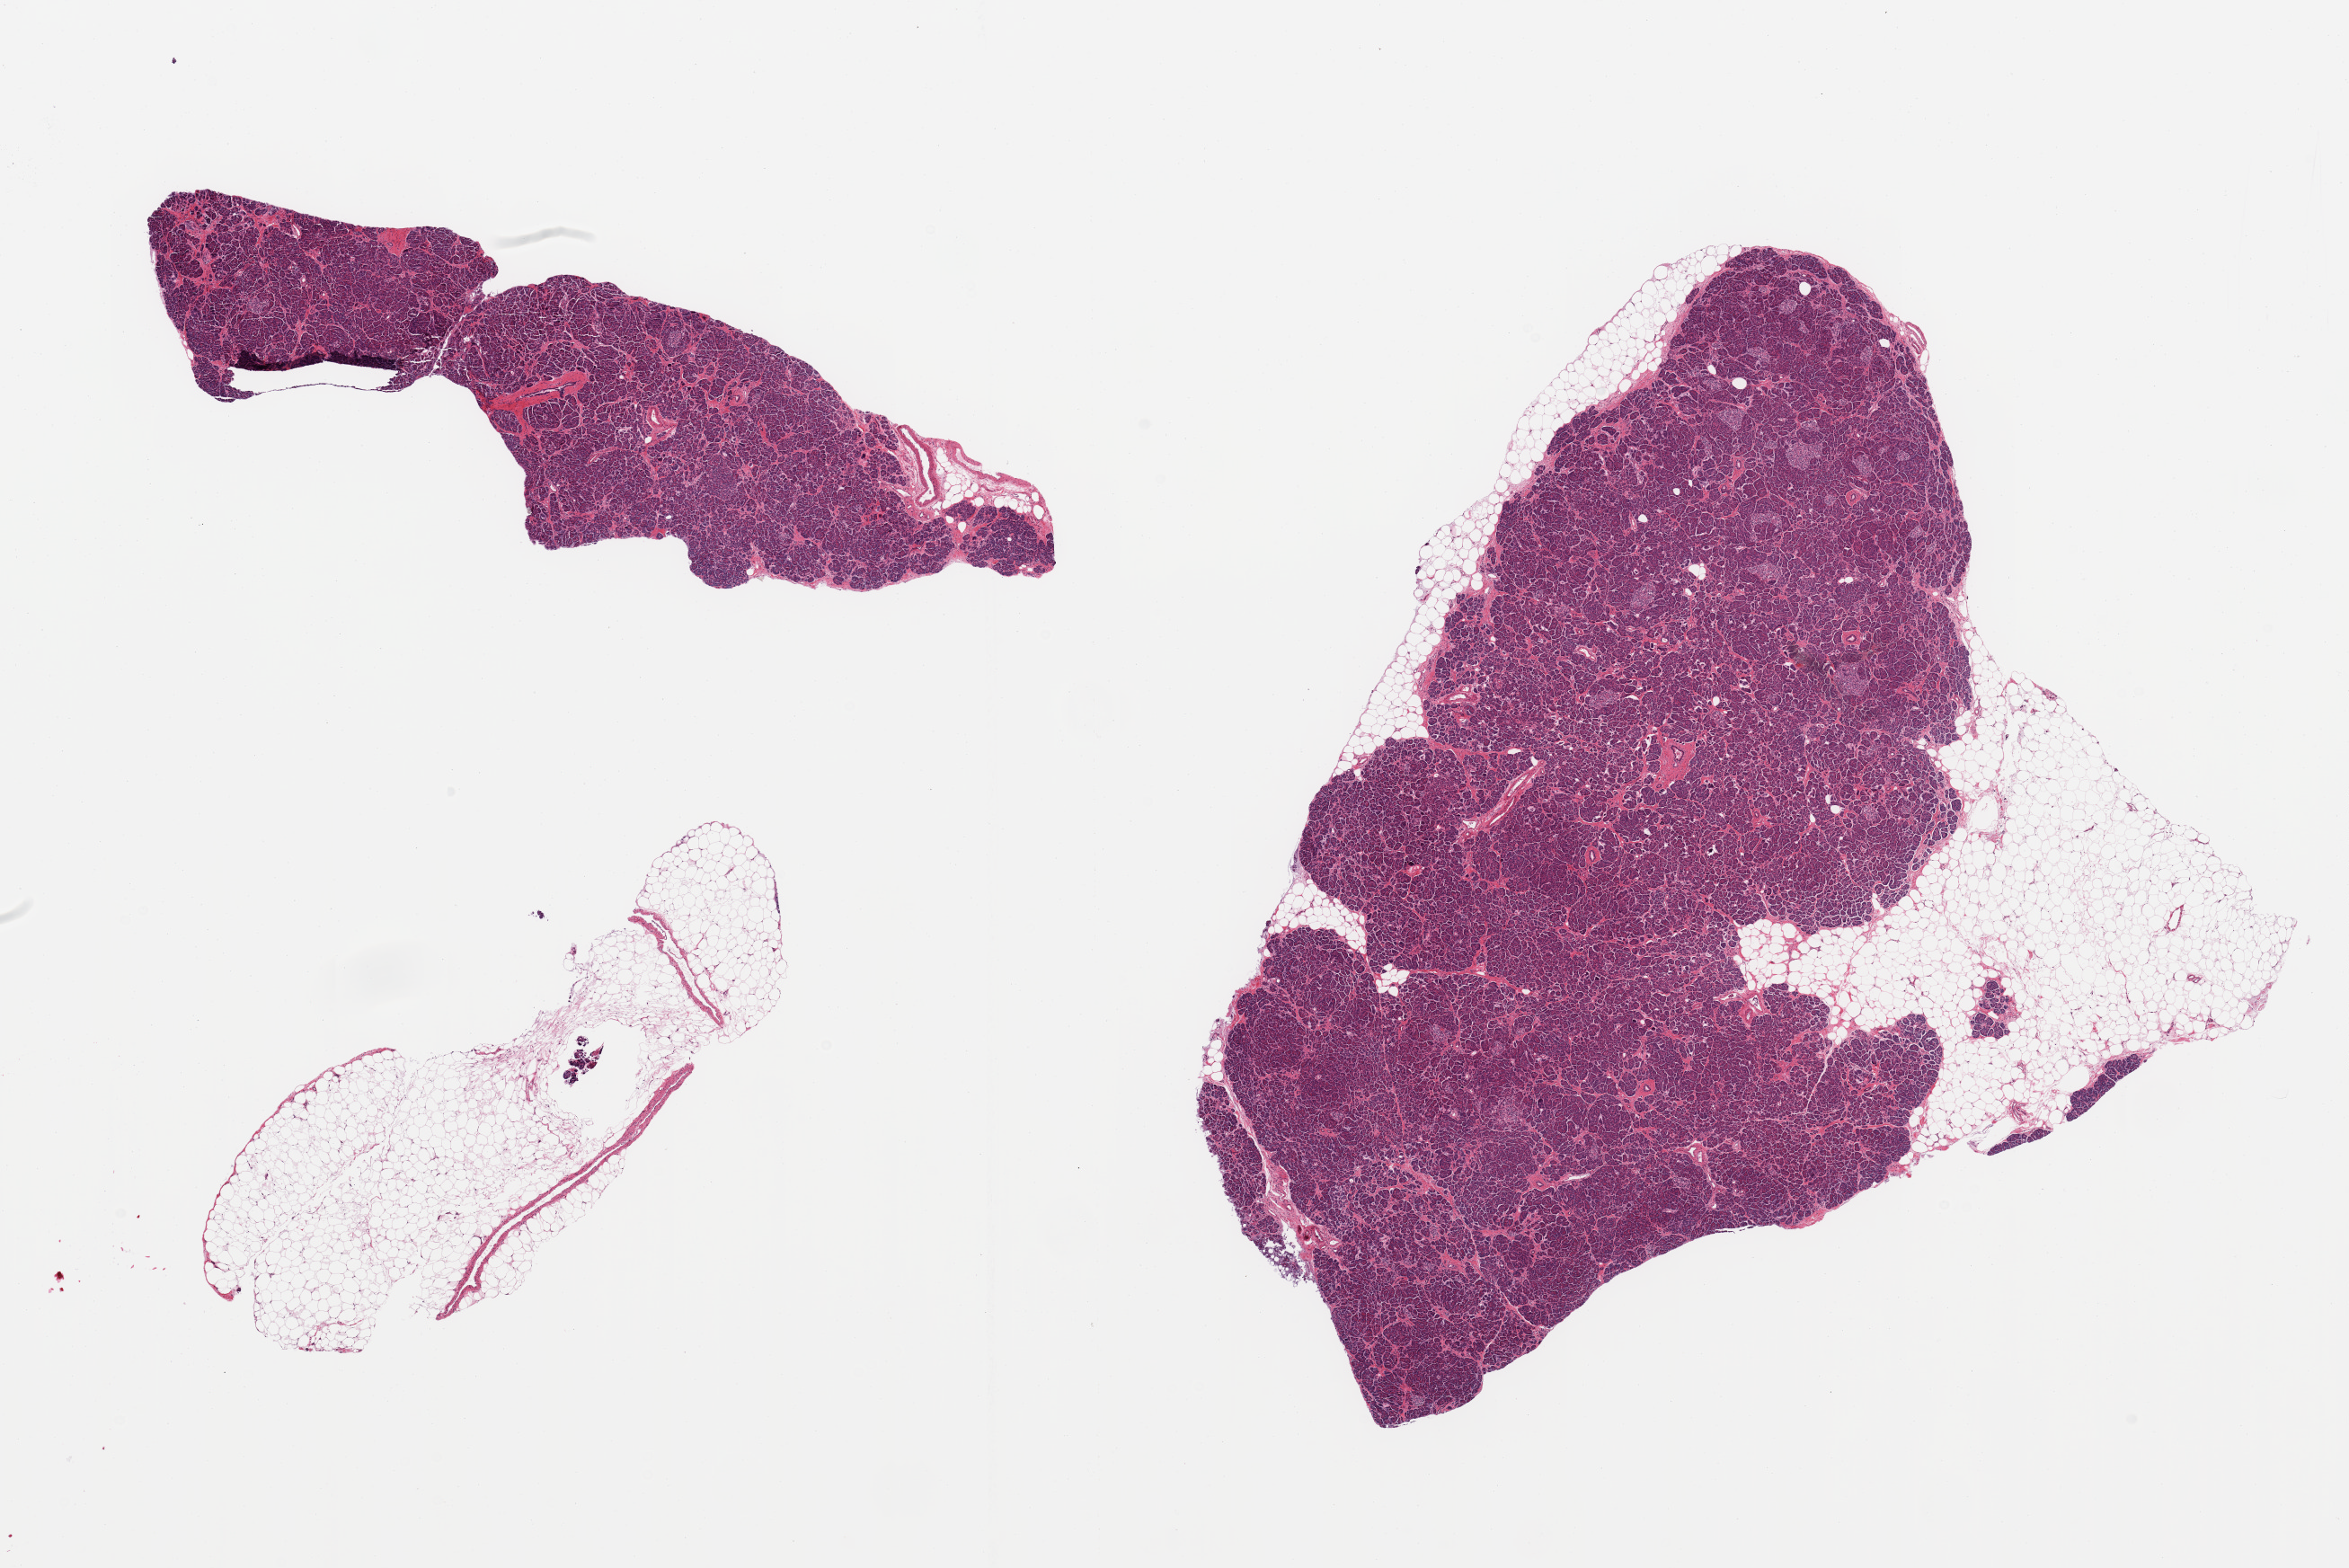
Digitized hematoxylin and eosin (H&E)-stained section, a low-resolution overview of the entire scanned area, about 20.7 x 13.8 mm (from a 20x scan), PAXgene-fixed paraffin-embedded (PFPE) section, target tissue: pancreas, donor tissue sample. Donor: male.
* reviewer comment on this tissue sample: 2 pieces plus a separate piece of fat; larger piece has up to 3mm external fat